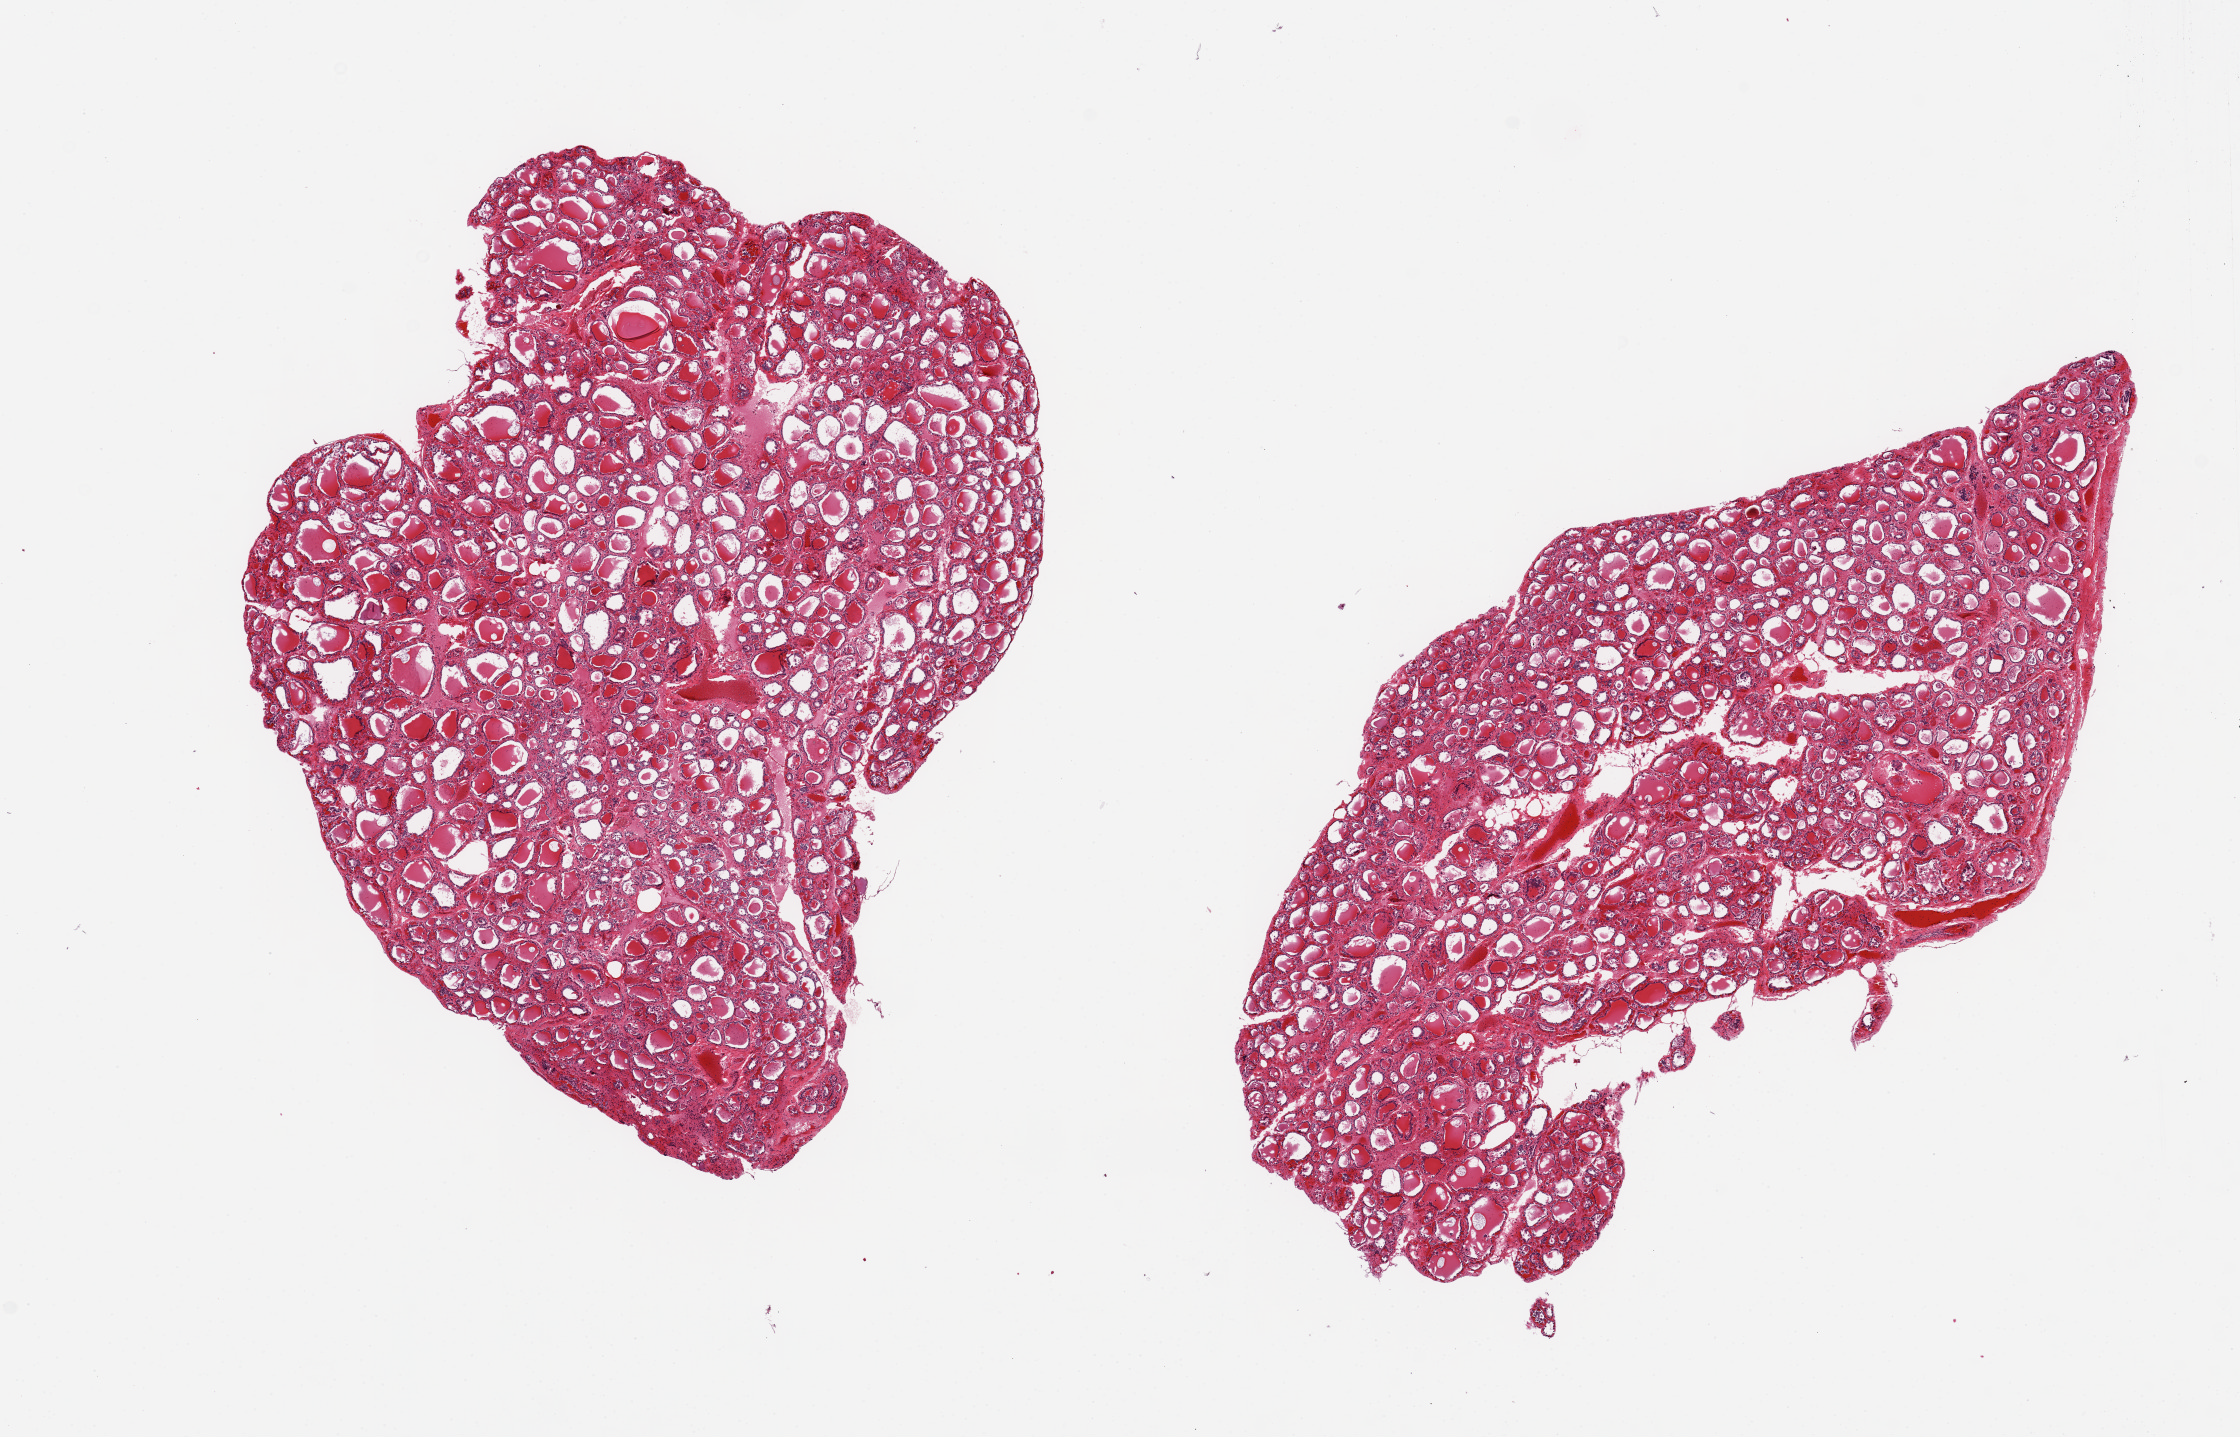
Digitized H&E-stained section — shown as a low-resolution overview of the whole scanned area (about 17.7 x 11.4 mm), PAXgene-fixed paraffin-embedded (PFPE) section, section of thyroid (target tissue), donor tissue sample. Donor: male.
- review note (as recorded): 2 pieces ~7x7 & 7x4mm; vascular congestion